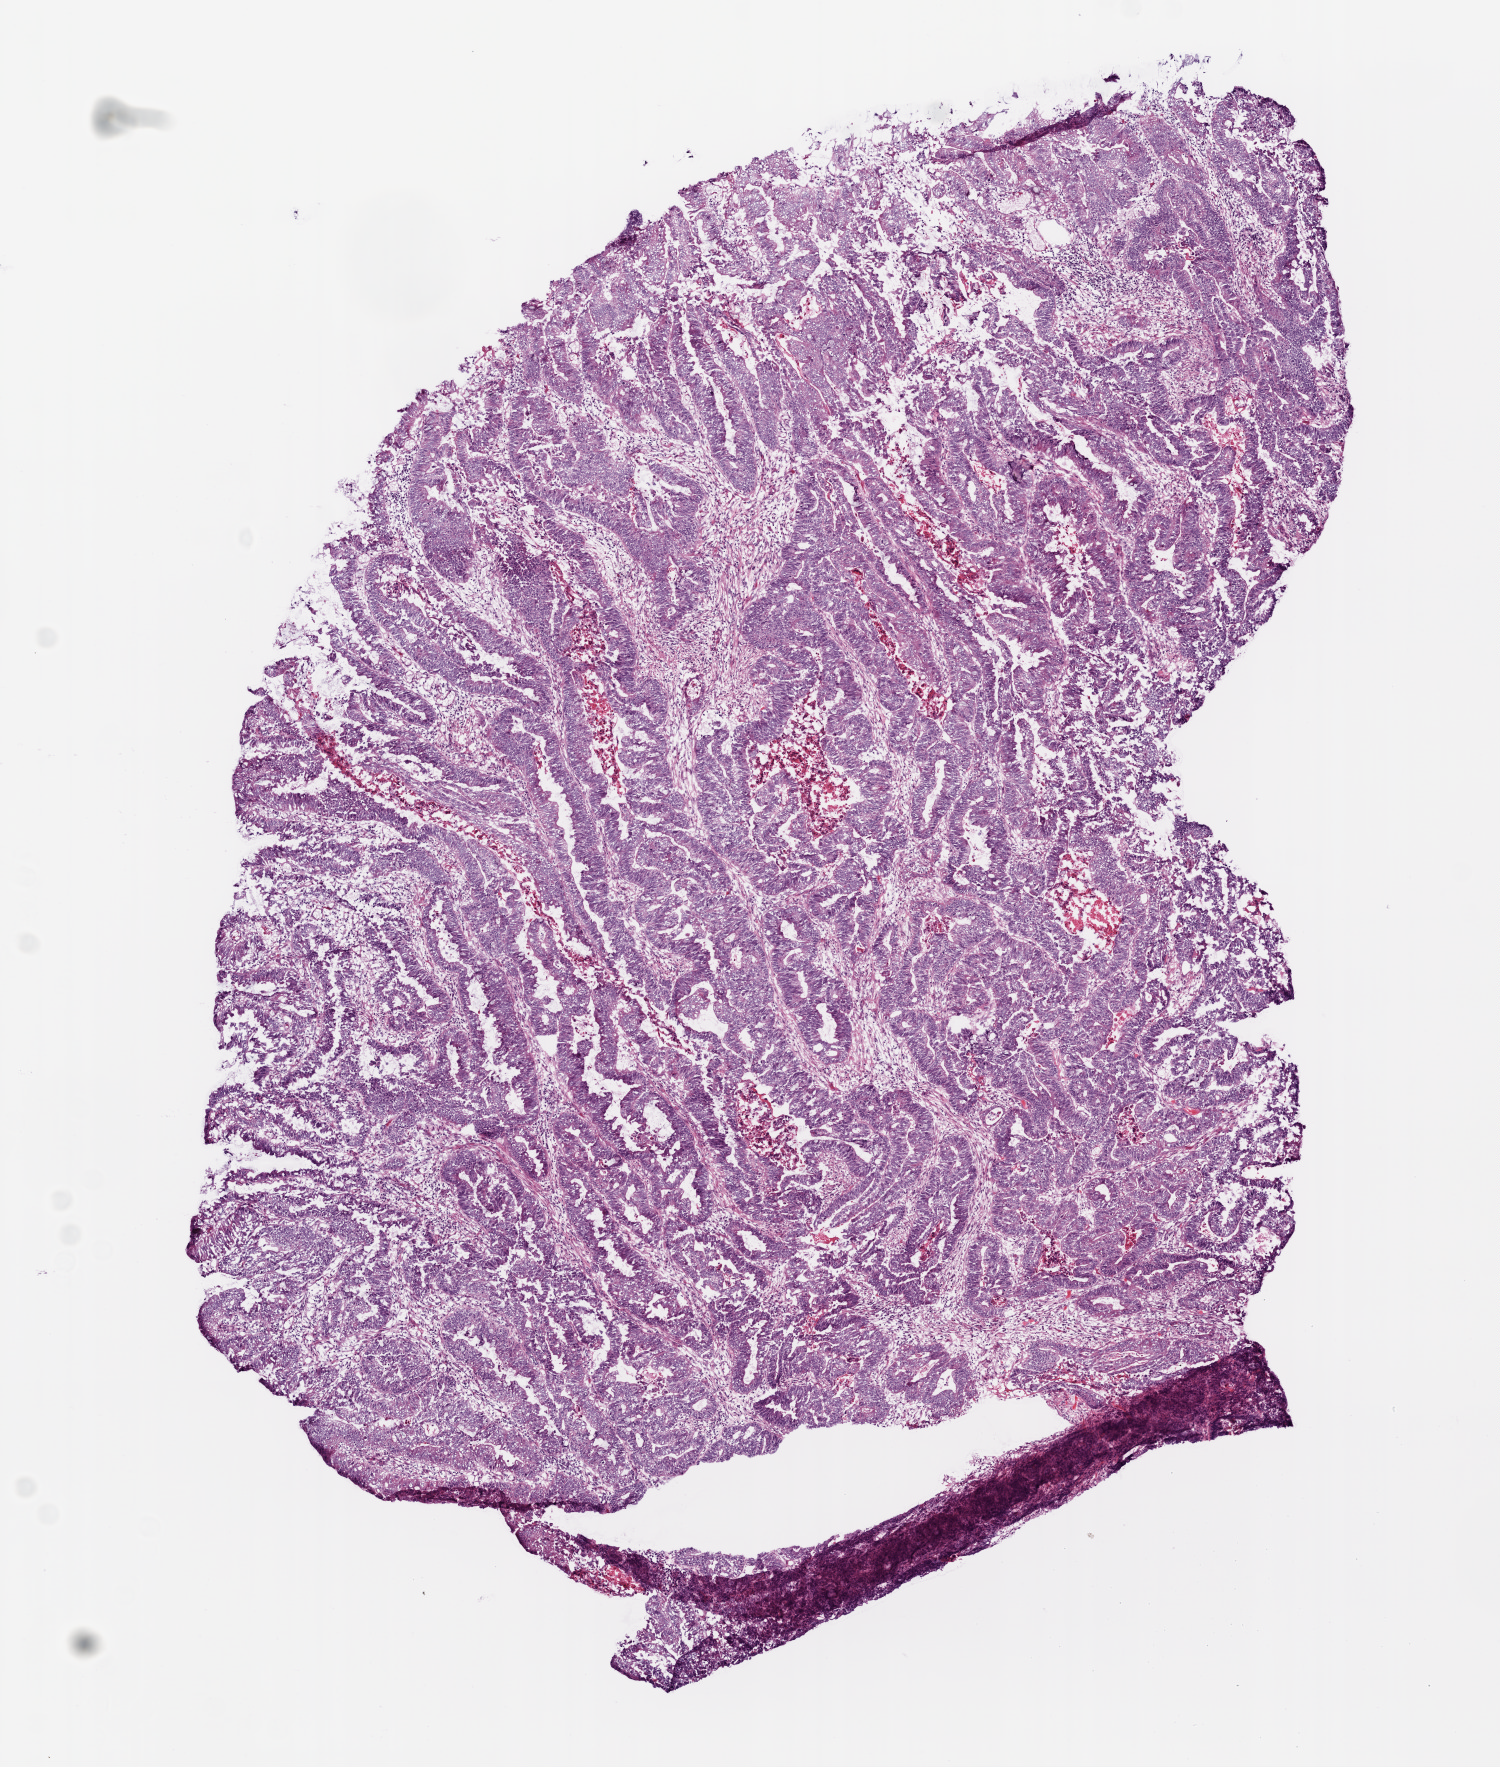
Digitized H&E tissue section (whole slide), low-resolution overview of the scanned area, about 6.0 x 7.1 mm (slide scanned at 20x). Frozen section from the top of the tissue portion. Colon, primary tumour sample. Male patient; age at initial diagnosis 83 years. Composition of this section per pathologist review: tumour cells 55%, tumour nuclei 75%, normal cells 20%, stromal cells 20%, necrosis 5%.
Lymph nodes positive (case pathology): 0 of 40 examined. Histologic diagnosis: Adenocarcinoma, NOS. AJCC pathologic stage: IIA (6th edition).